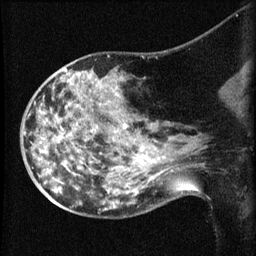
Breast MRI (dynamic contrast-enhanced), one sagittal slice; dynamic contrast-enhanced series, image 2 of 3 at this slice position (ordered by acquisition); 1.5 T; TE 4.2 ms, TR 8.2 ms; 2.1 mm slice thickness; 256 × 256 image matrix, field of view 180 × 180 mm. Female patient, age 50 years.
Structures marked on this image (semi-automatic segmentation, software-assisted and operator-edited):
- analysis volume of interest (the breast-tissue region the enhancement analysis was run in; not a lesion): box from (x=38, y=74) to (x=169, y=211) px
- tumour enhancement mask (voxels above the 70 % enhancement threshold inside the analysis volume of interest): (x=123, y=123)–(x=158, y=179)